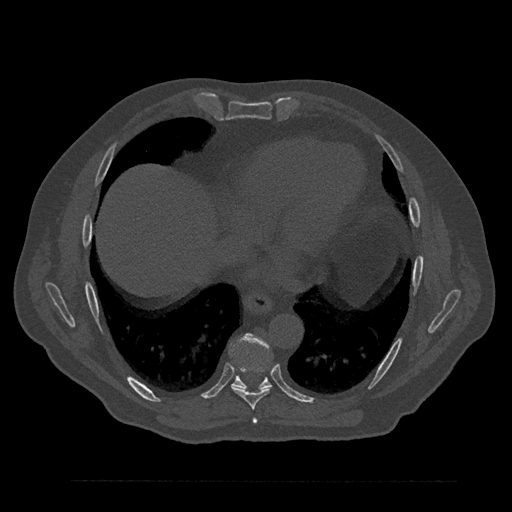
CT including the spine, one axial slice. Slice 436 of 797 in the series (ordered by position). 120 kVp. Bone window (W 1800 / L 400 HU). 512 × 512 image matrix, field of view 430 × 430 mm. Male patient, age 61 years. Case-level facts recorded for this patient, not image findings: primary cancer: prostate.
Annotated regions visible in this slice (semi-automatically segmented with operator editing):
- T7 vertebra: bounding box [x1, y1, x2, y2] px = [252, 418, 257, 424]
- T8 vertebra: [231, 367, 272, 410]
- T9 vertebra: [230, 334, 272, 389]